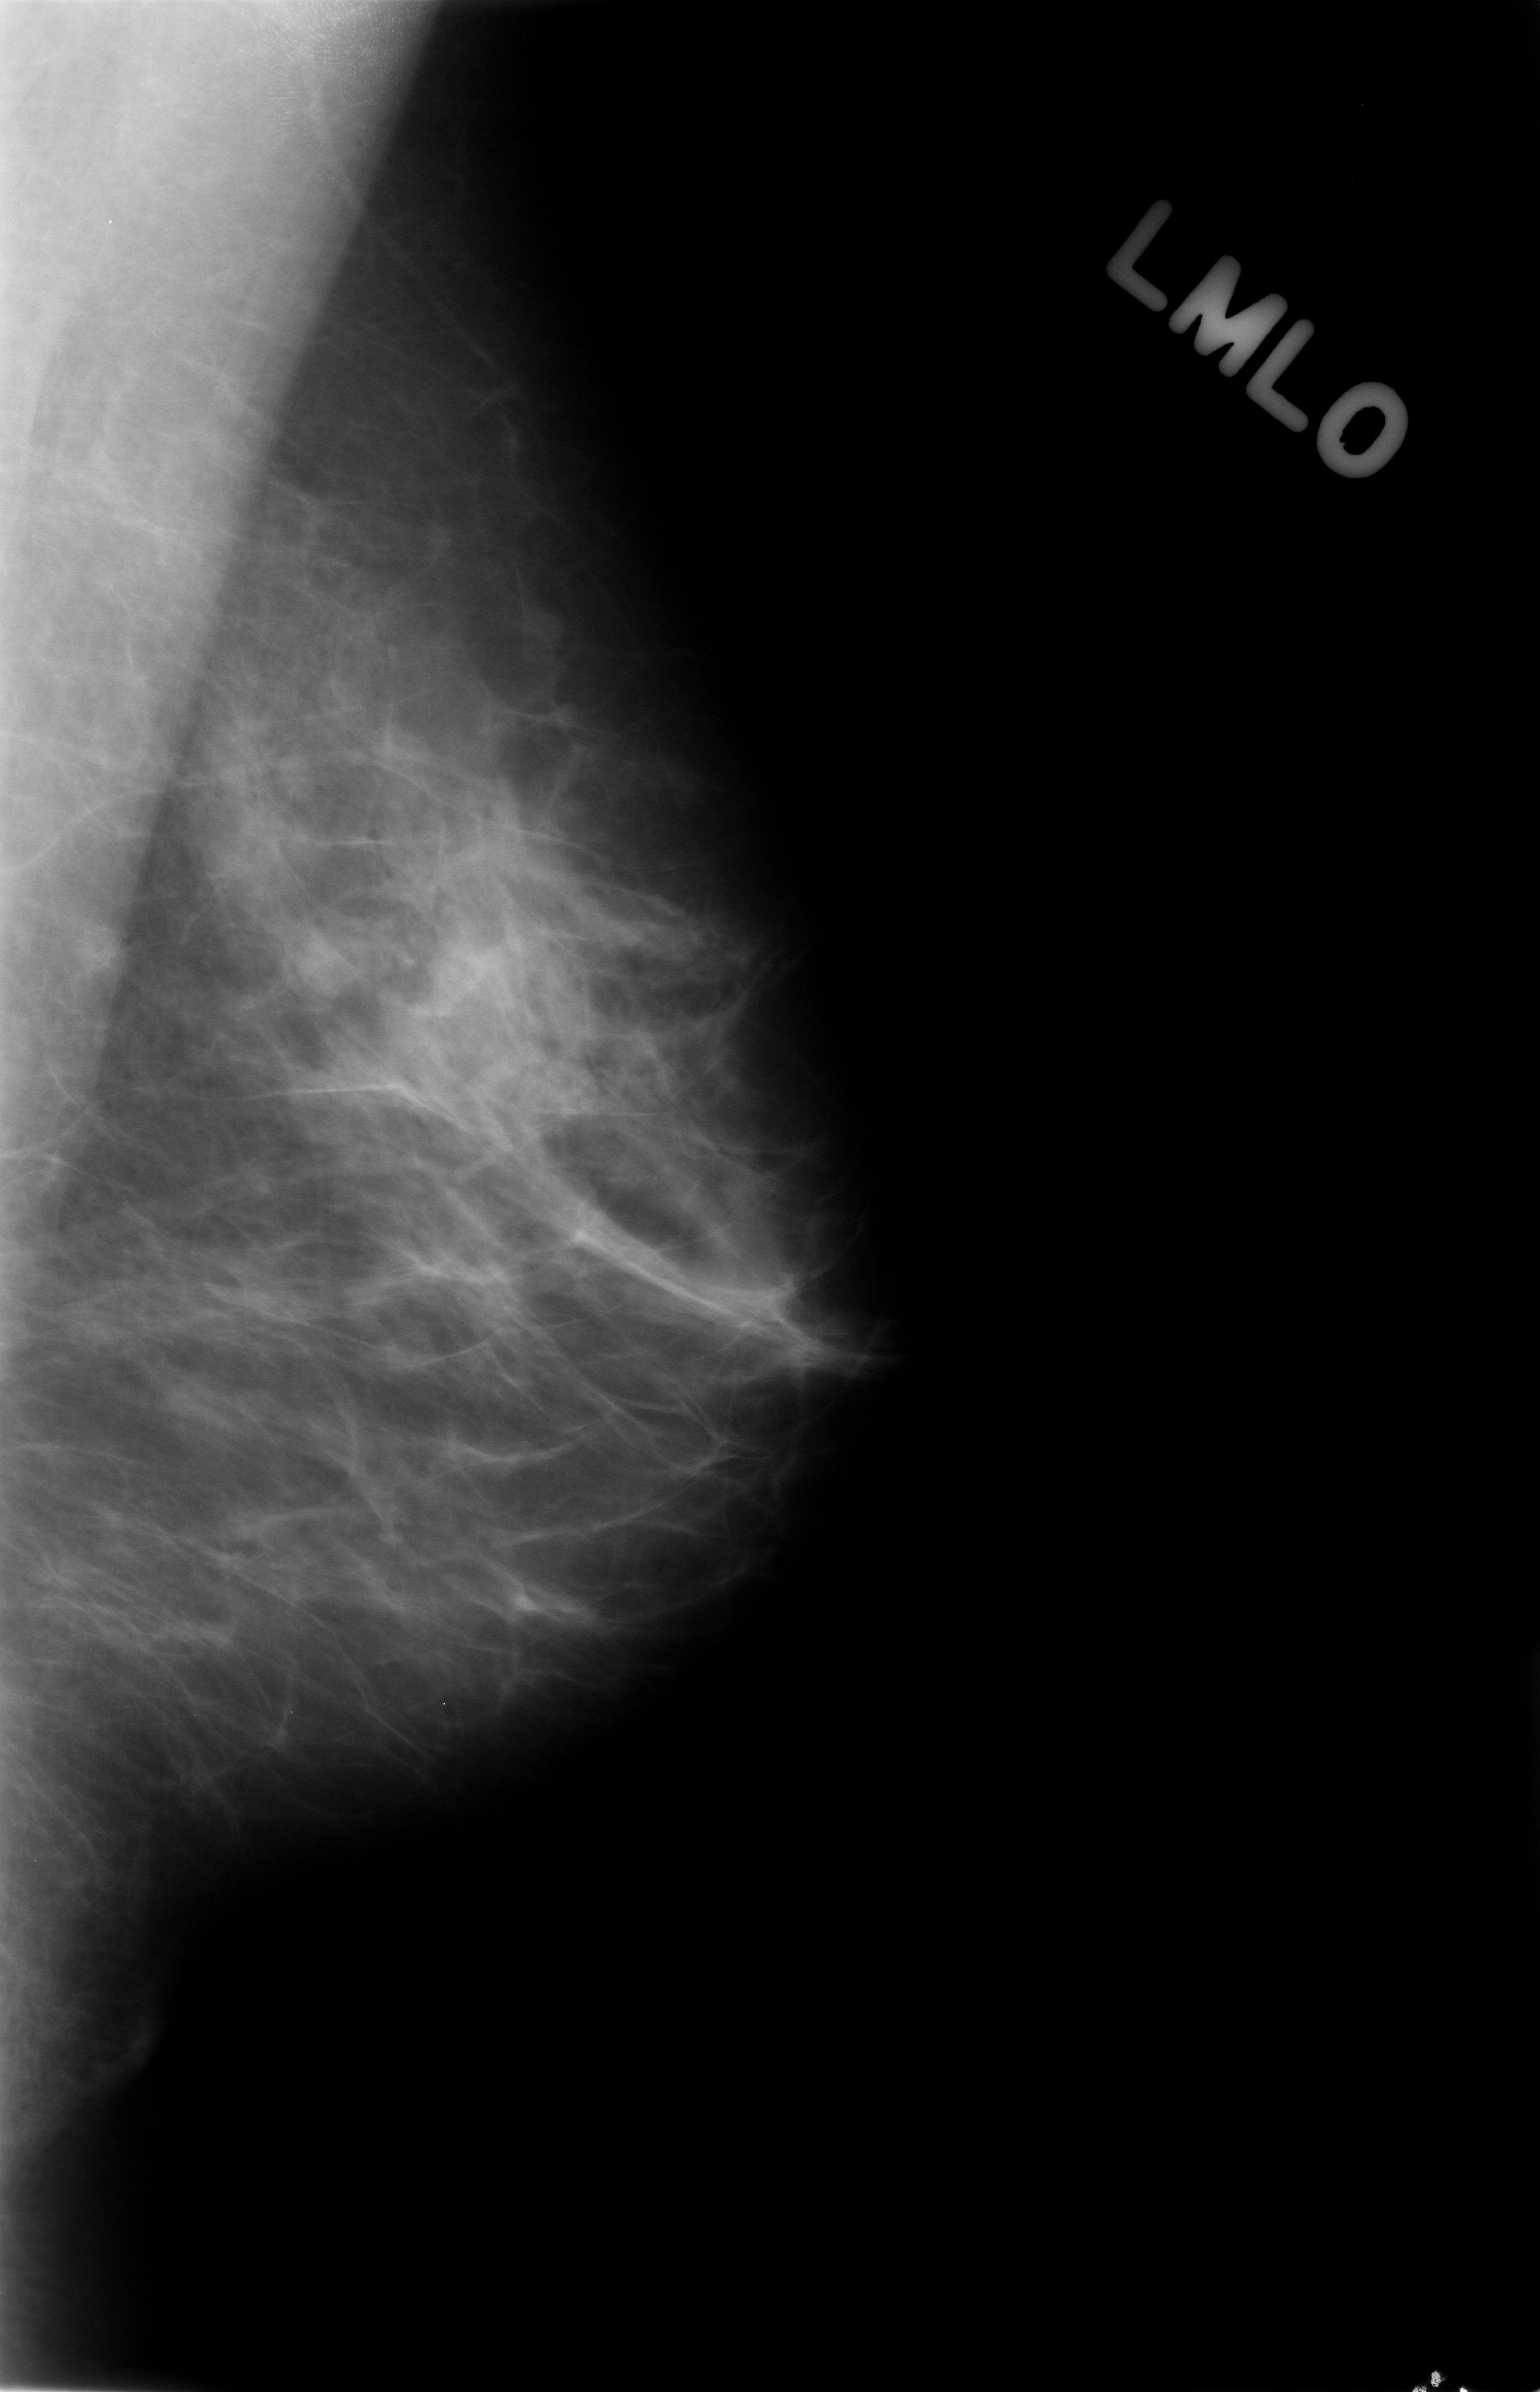
Digitized screen-film mammogram. Left breast. Mediolateral oblique (MLO) view. BI-RADS breast density category 2 (scale 1–4). 1540 × 2392 image matrix.
Expert-marked regions of interest on this film, with their recorded descriptors:
- mass, shape asymmetric breast tissue; BI-RADS assessment category 3; subtlety rating 3 on a 1 (subtle) to 5 (obvious) scale; benign; no additional work-up was recommended (outcome (as recorded, no biopsy): benign without callback): box from (x=200, y=740) to (x=383, y=960) px